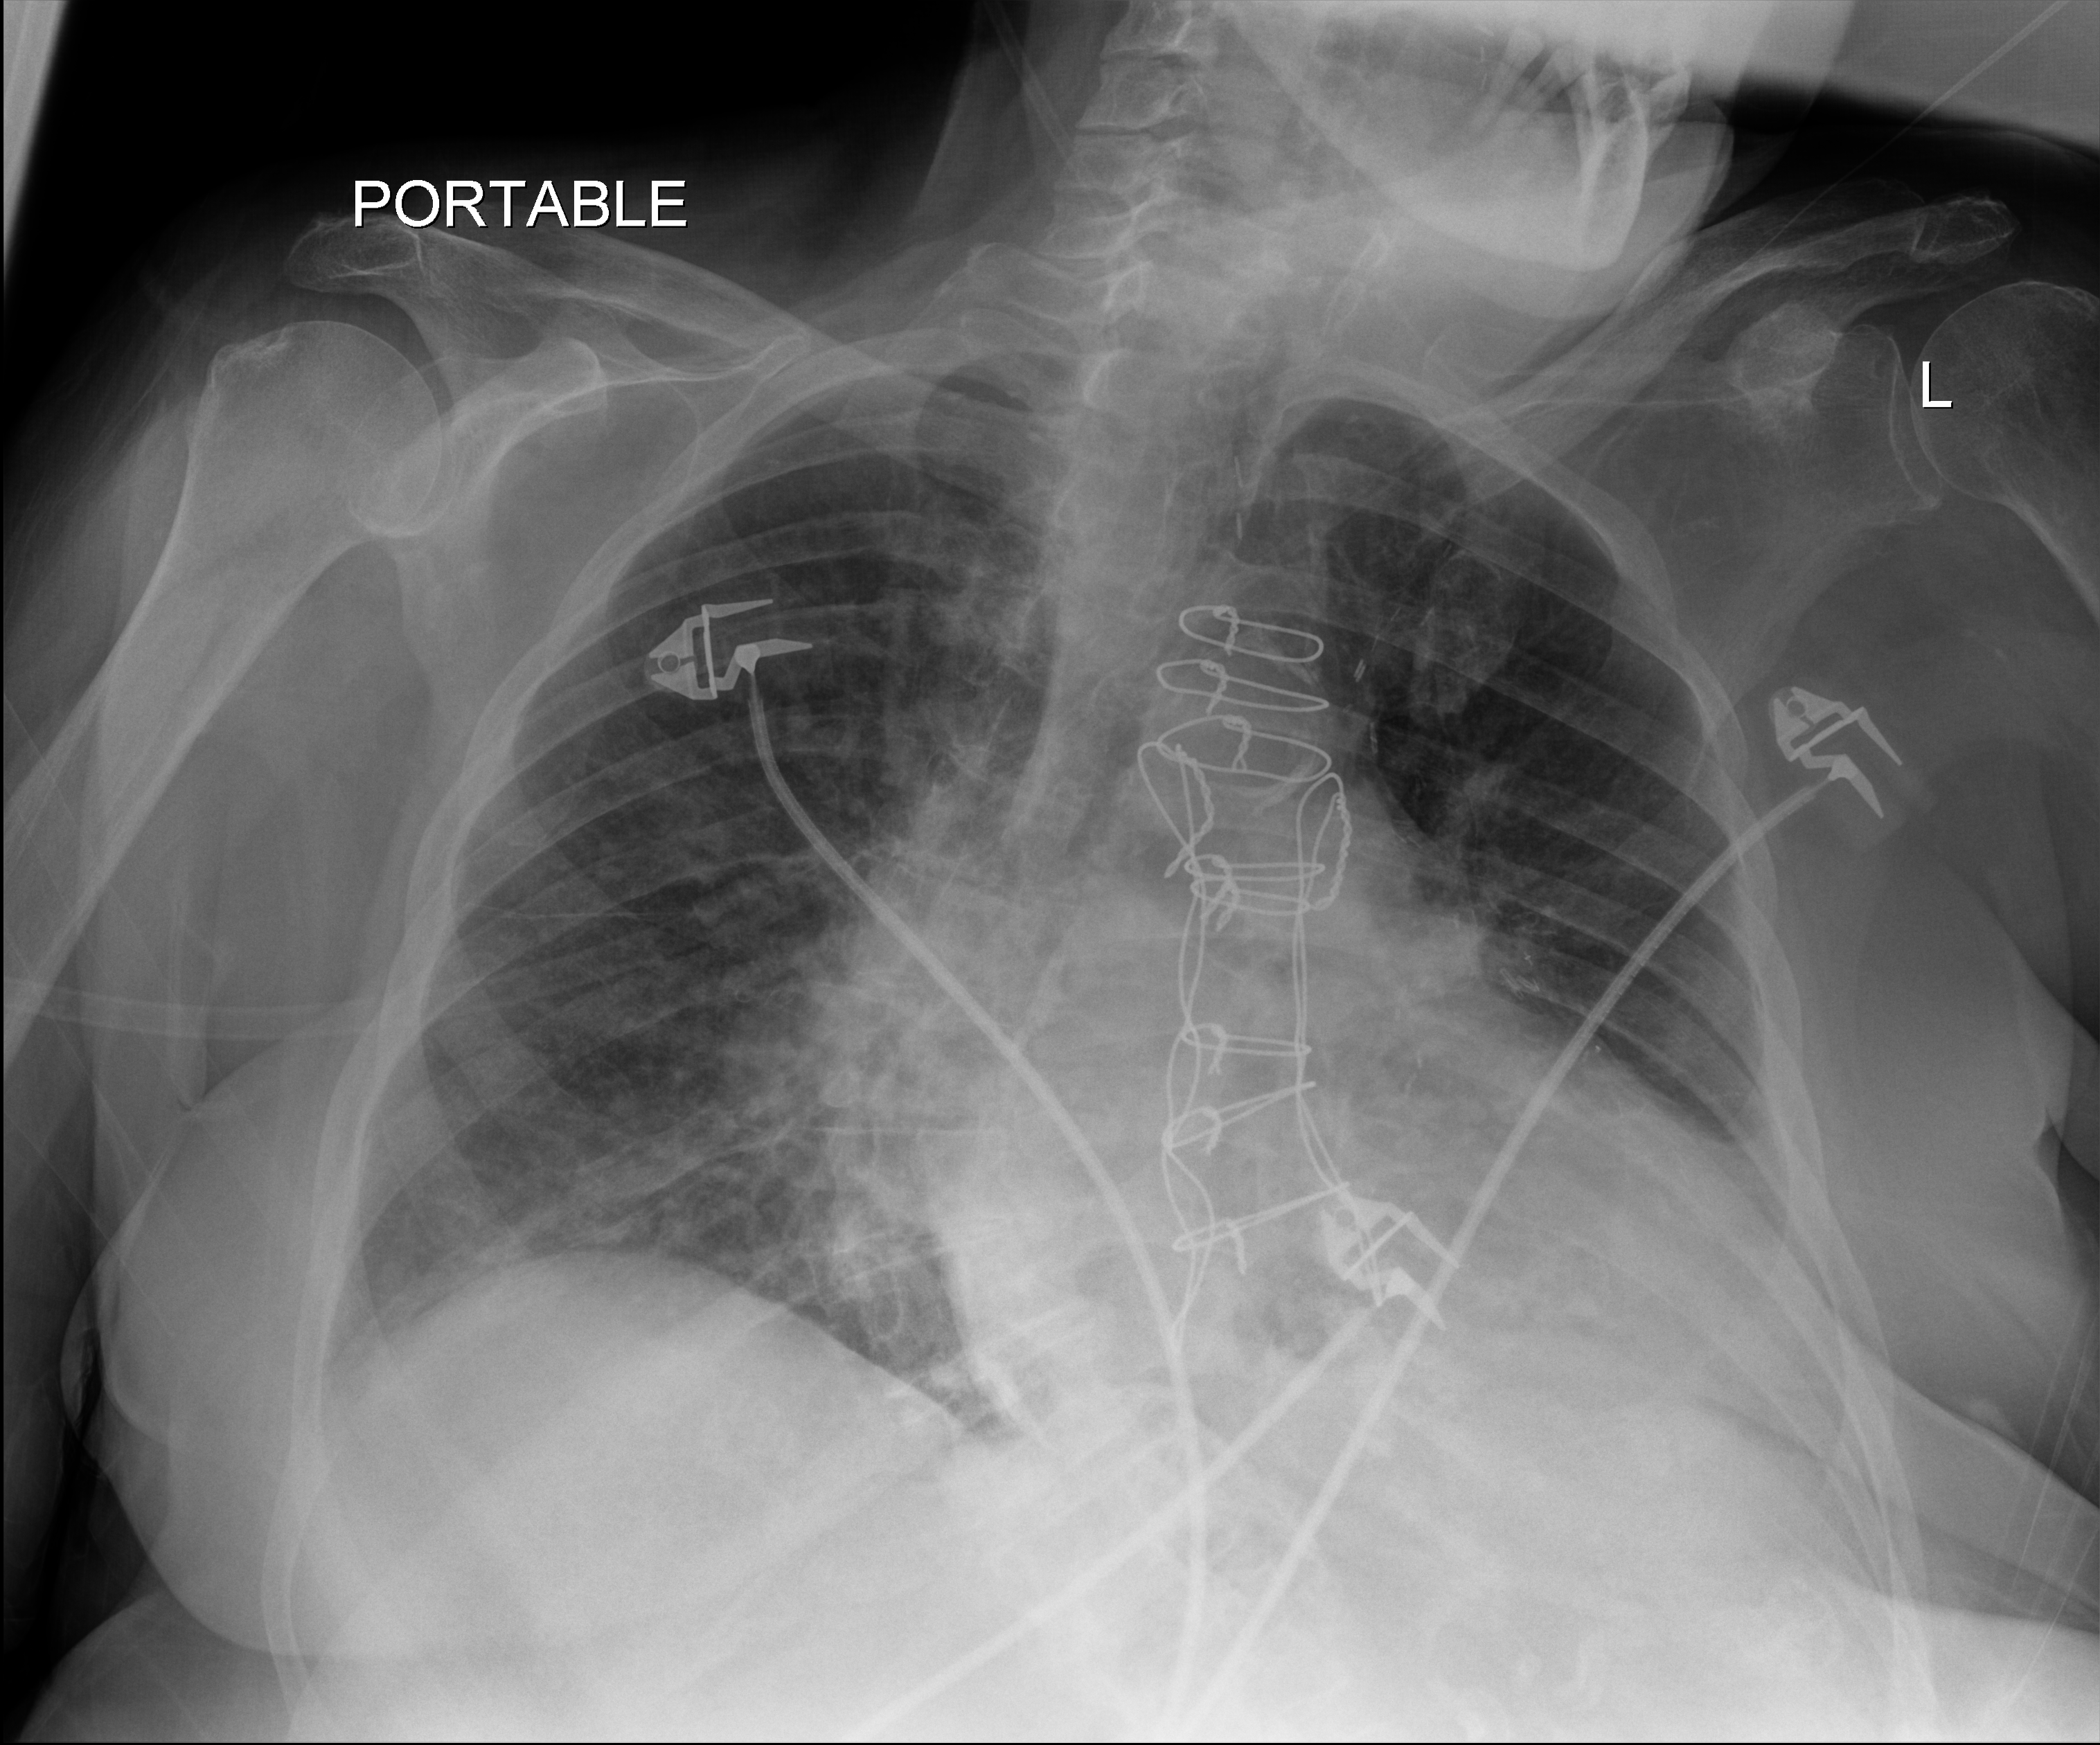
Chest X-ray; anteroposterior (AP) projection. Patient hospitalised with COVID-19; female, aged 75–90 years.
Admission-level facts for this patient (not findings on this image; timing relative to this image not recorded):
- admitted to intensive care during this hospital stay: no